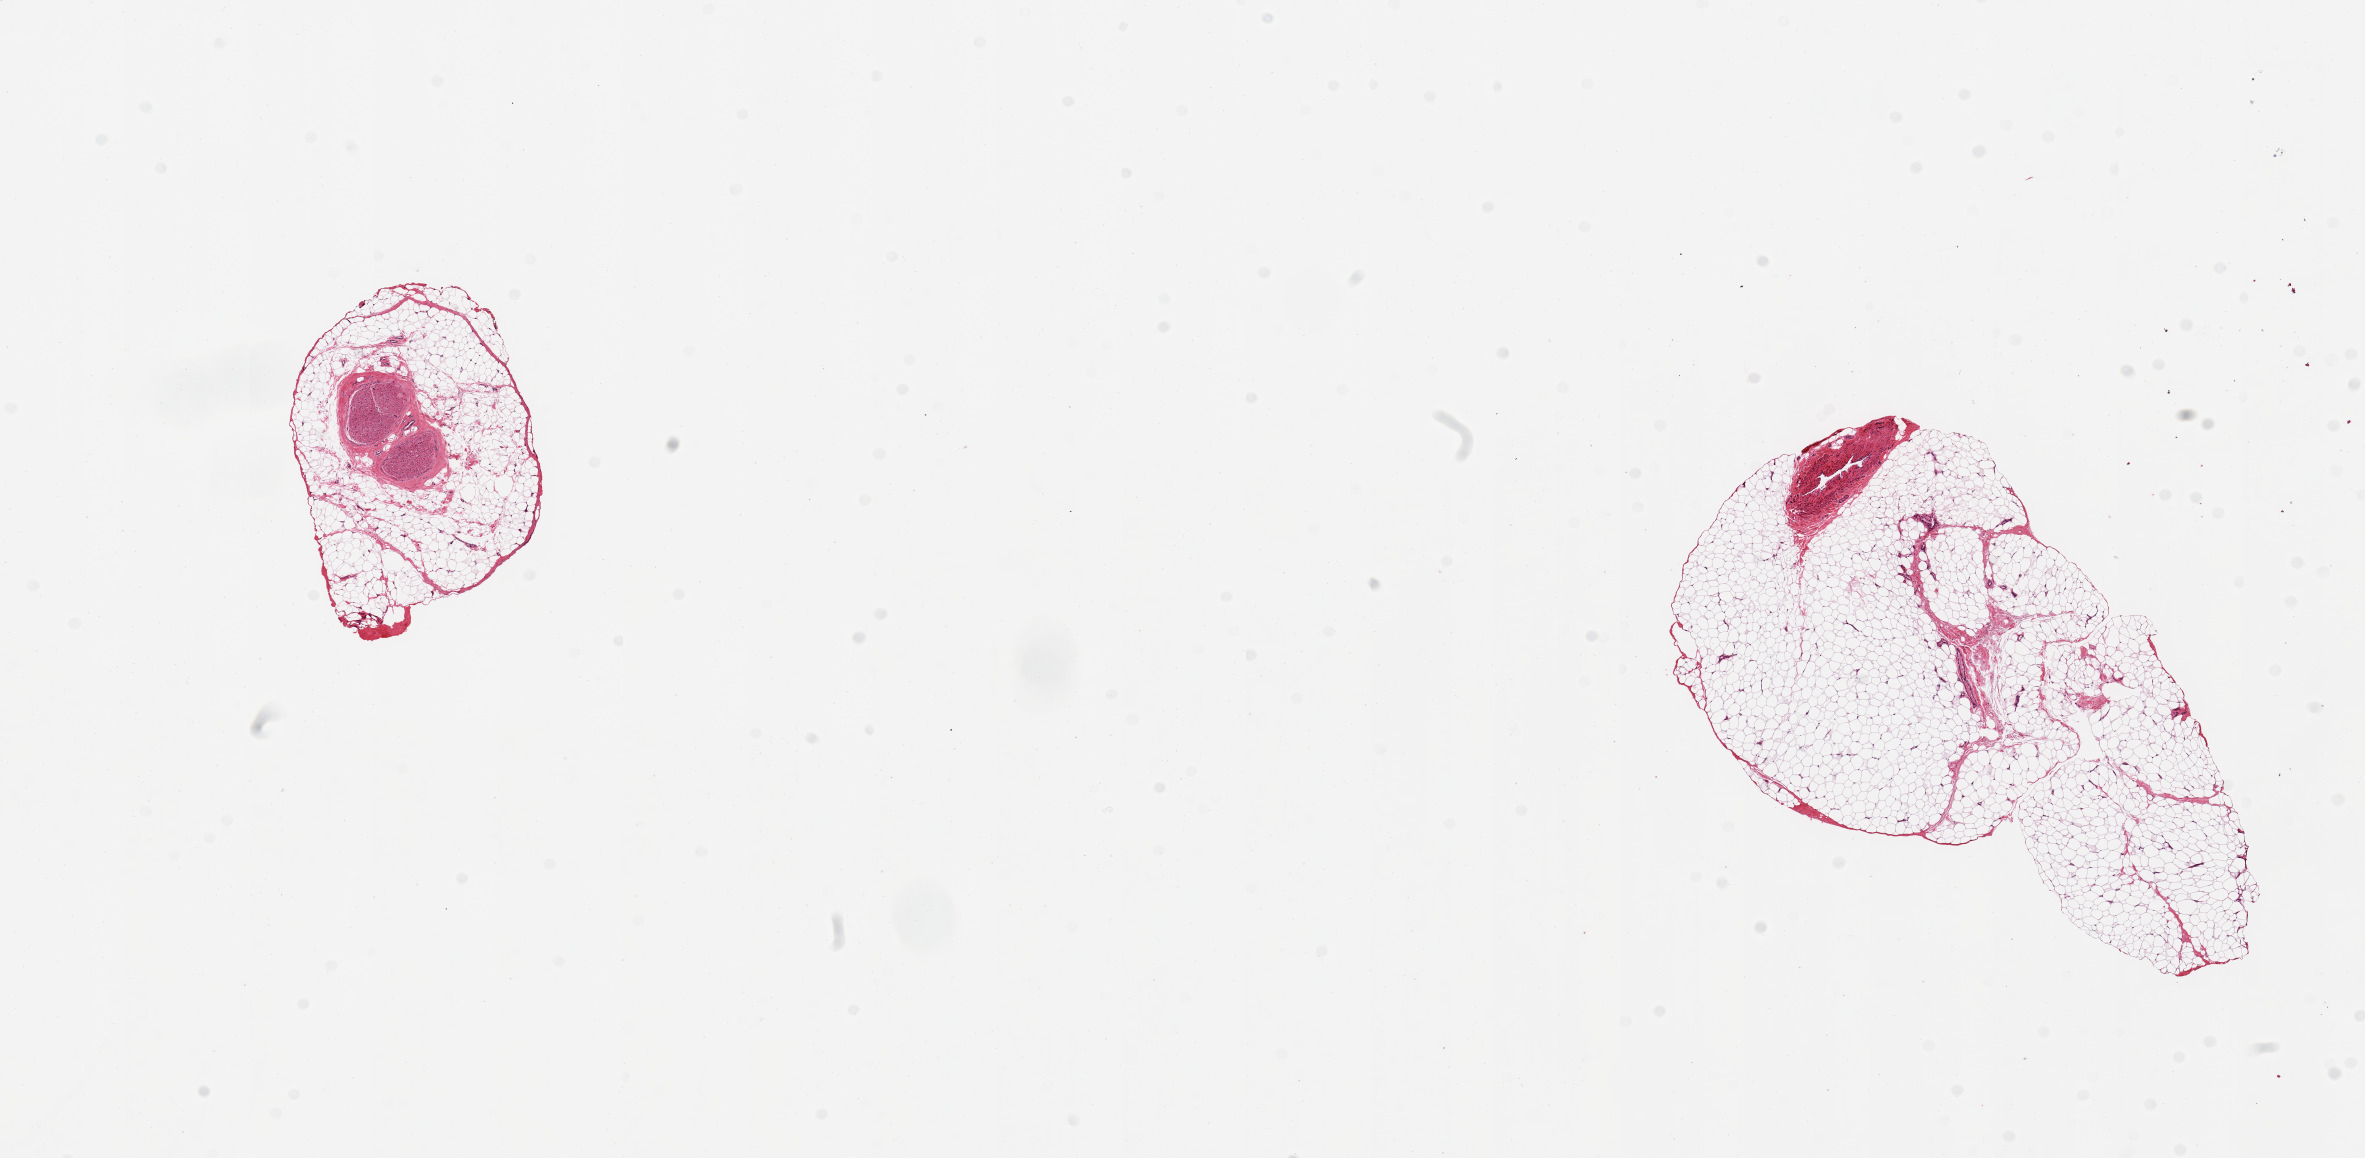
Whole-slide image, haematoxylin and eosin stain, brightfield, a low-resolution overview of the entire scanned area, about 18.7 x 9.2 mm, PAXgene-fixed, paraffin-embedded tissue, sampled site (target tissue): tibial artery, tissue donor sample. Donor sex: male.
- review note (as recorded): Not artery. One piece of peripheral nerve; one piece fat with minute vein (0.2x0.6mm